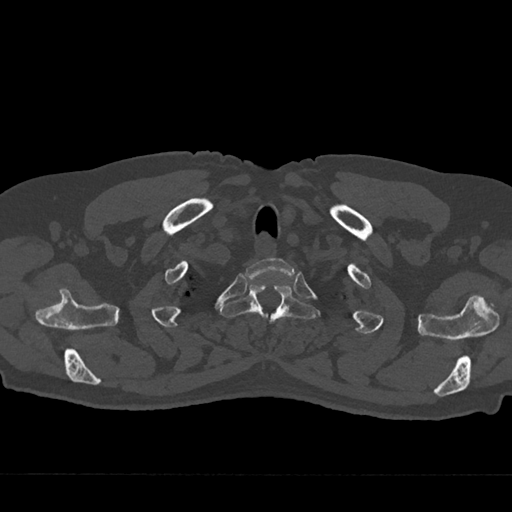
CT including the spine, one axial slice; position 626 of 797 along the scan axis; reconstruction kernel Br40s/3; bone window (W 1800 / L 400 HU); 0.5 mm slice thickness; 512 × 512 image matrix, field of view 377 × 377 mm. Male patient, age 75 years. From the clinical record (not read from this slice): primary cancer: renal.
Annotated regions visible in this slice (semi-automatically segmented with operator editing):
- T1 vertebra: bounding box [x1, y1, x2, y2] px = [245, 258, 294, 281]
- T2 vertebra: [220, 284, 319, 324]